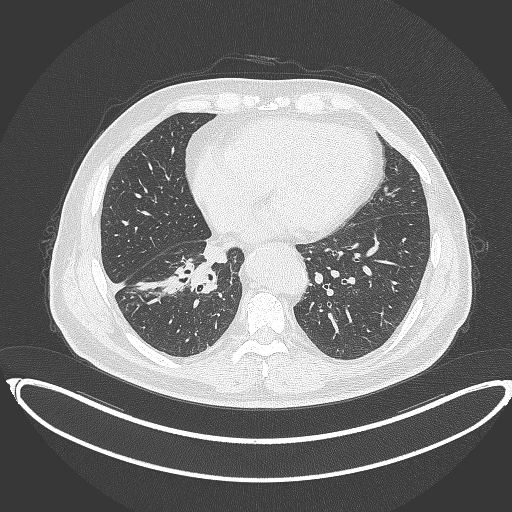
Chest CT, one axial slice; slice 152 of 387 in the series (ordered by position); lung window (W 1500 / L -600 HU); 512 × 512 image matrix, field of view 448 × 448 mm. Male patient, age 61 years. Case-level facts recorded for this patient, not image findings: clinical TNM (as recorded): T1b N1 M0.
Structures marked on this image (rectangle marked by the reading radiologist):
- lung tumour (recorded histology: squamous cell carcinoma): bounding box [x1, y1, x2, y2] px = [161, 252, 217, 300]